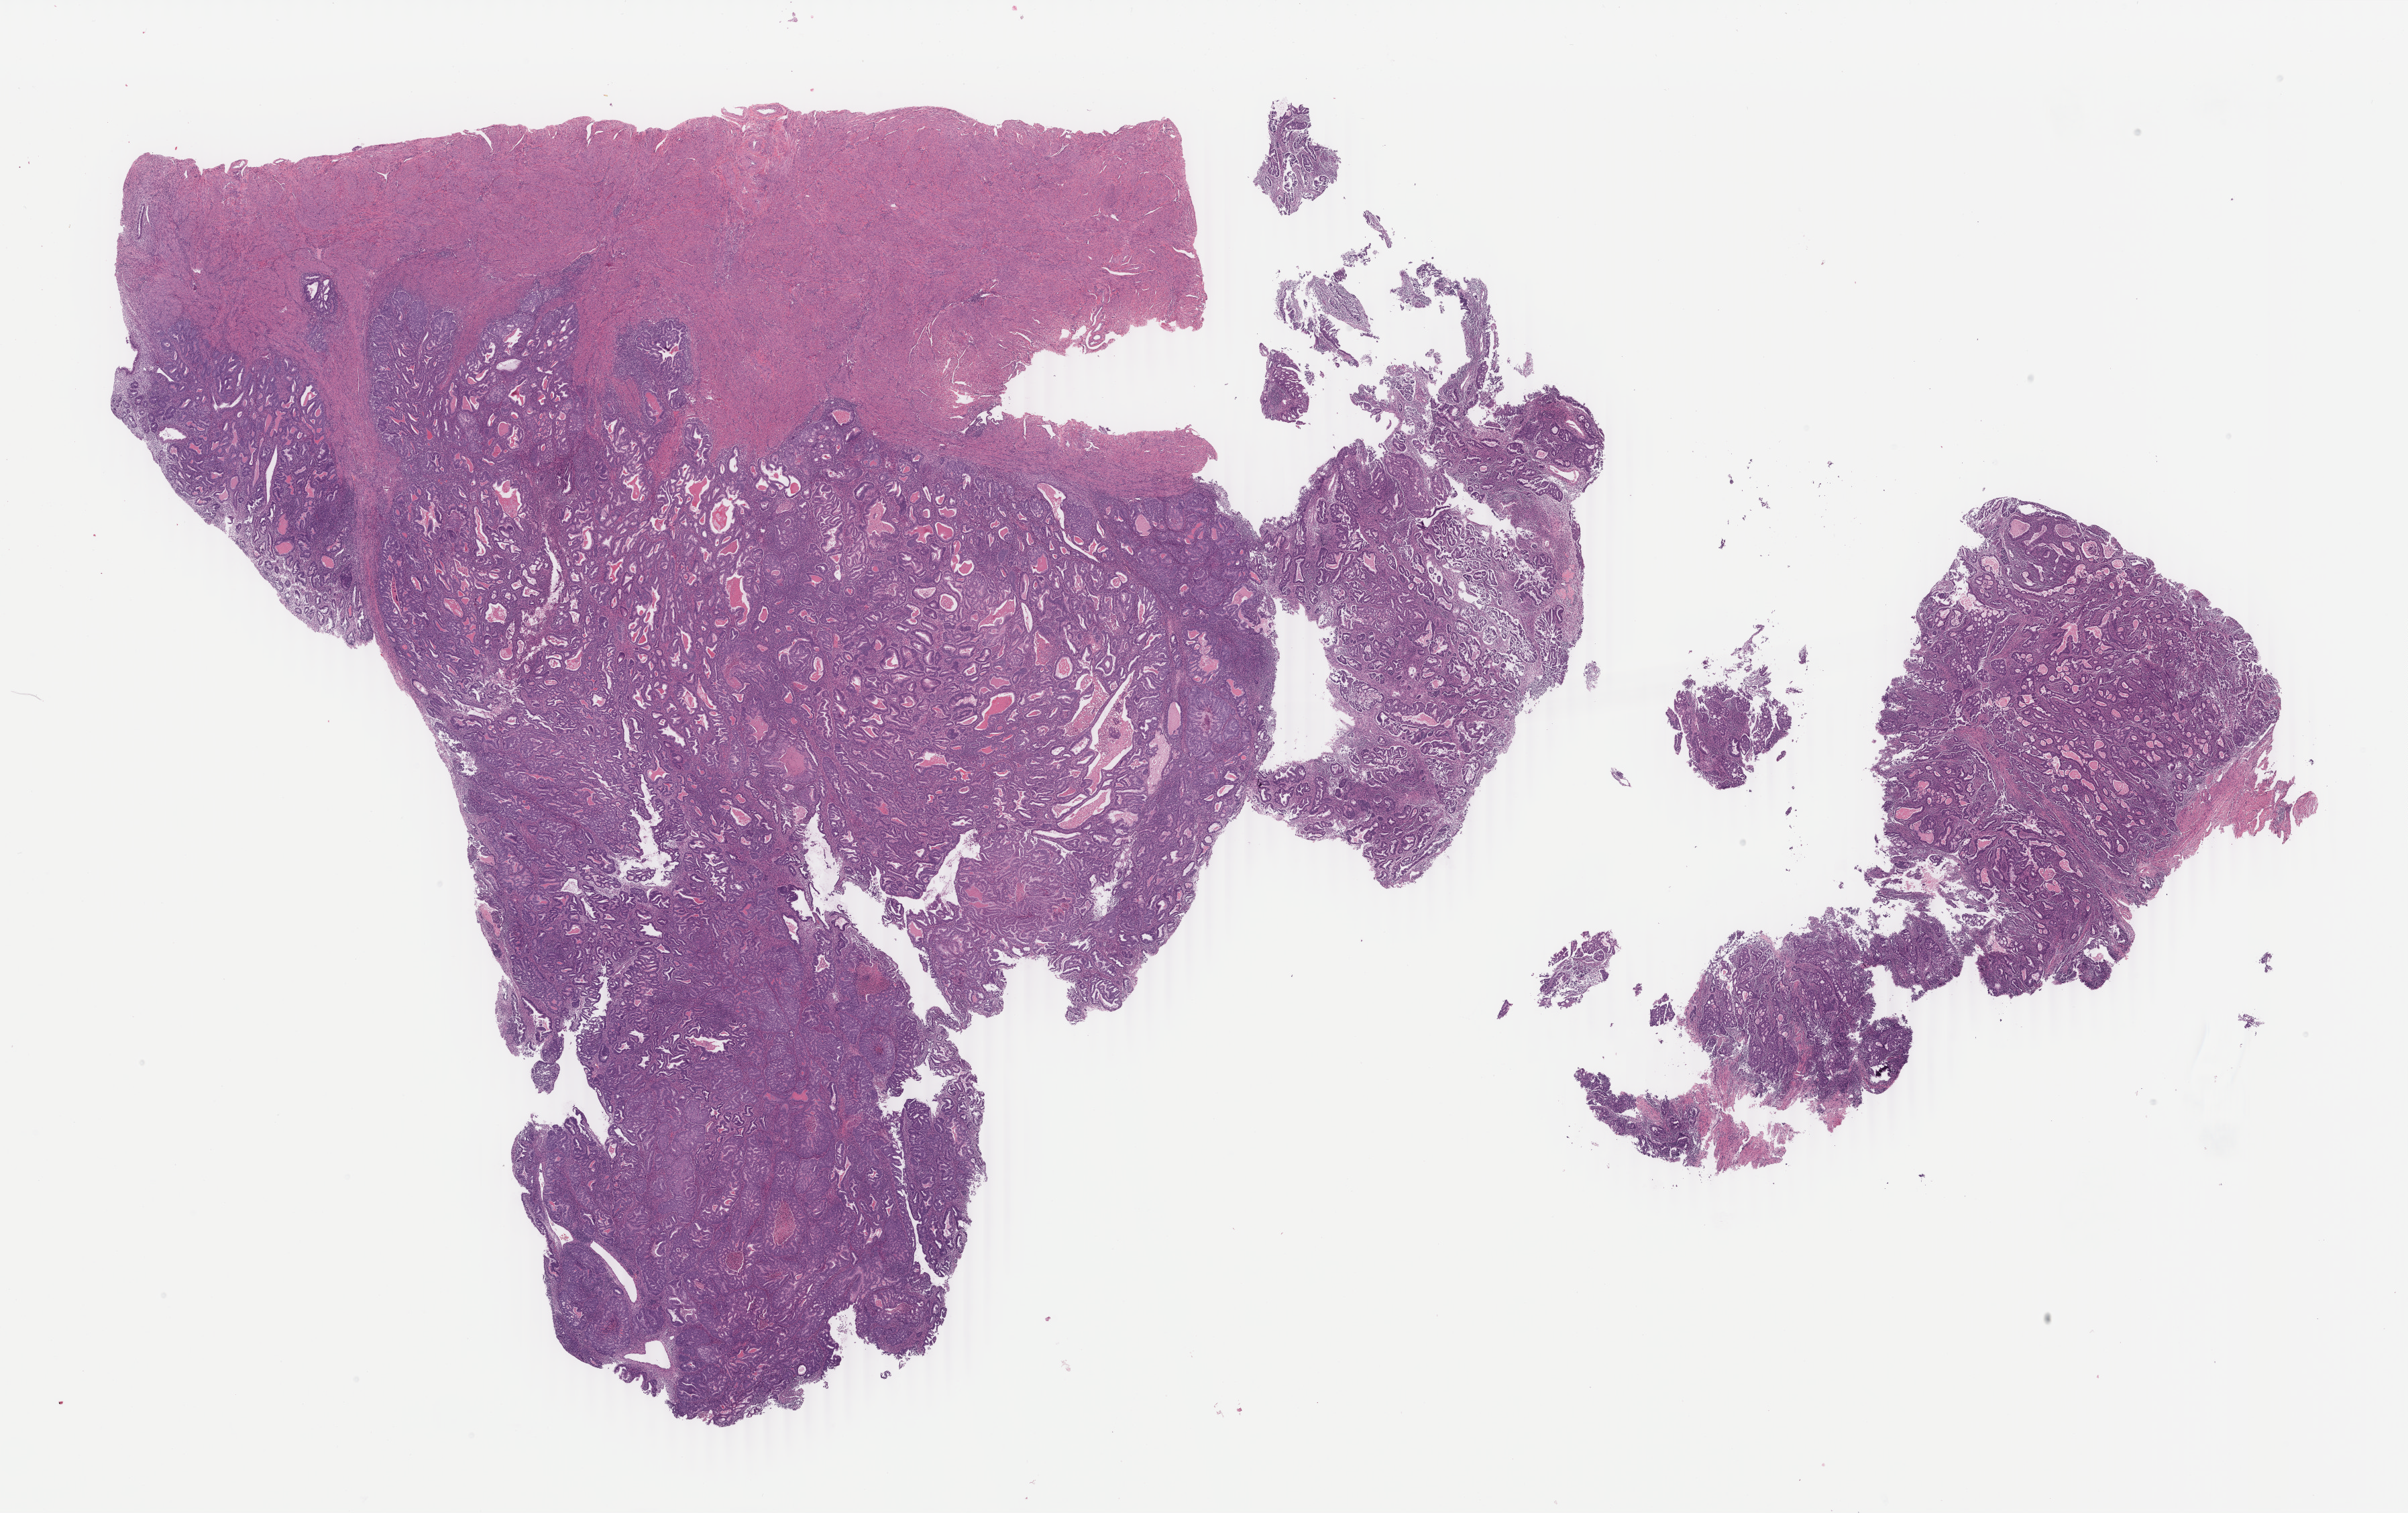
Hematoxylin and eosin (H&E) stained whole-slide image, whole scanned area (about 28.6 x 17.9 mm) shown as a low-resolution overview; FFPE section; sample: primary tumour, uterus. Patient: female, age at initial diagnosis 51 years. Histologic grade: G3 (poorly differentiated).
FIGO stage: IA. Diagnosis: Endometrioid adenocarcinoma, NOS.